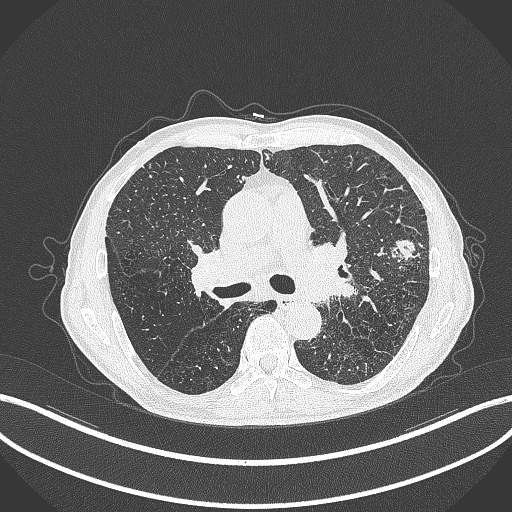
Chest CT, one axial slice. Position 256 of 463 along the scan axis. Reconstruction kernel B70f. 120 kVp. Lung window (W 1500 / L -600 HU). 512 × 512 image matrix, field of view 400 × 400 mm. Patient: male, 74 years. Case-level facts recorded for this patient, not image findings: clinical TNM (as recorded): T2a N1 M0.
Annotated regions visible in this slice (rectangle marked by the reading radiologist):
- lung tumour (recorded histology: adenocarcinoma): box from (x=389, y=237) to (x=421, y=265) px